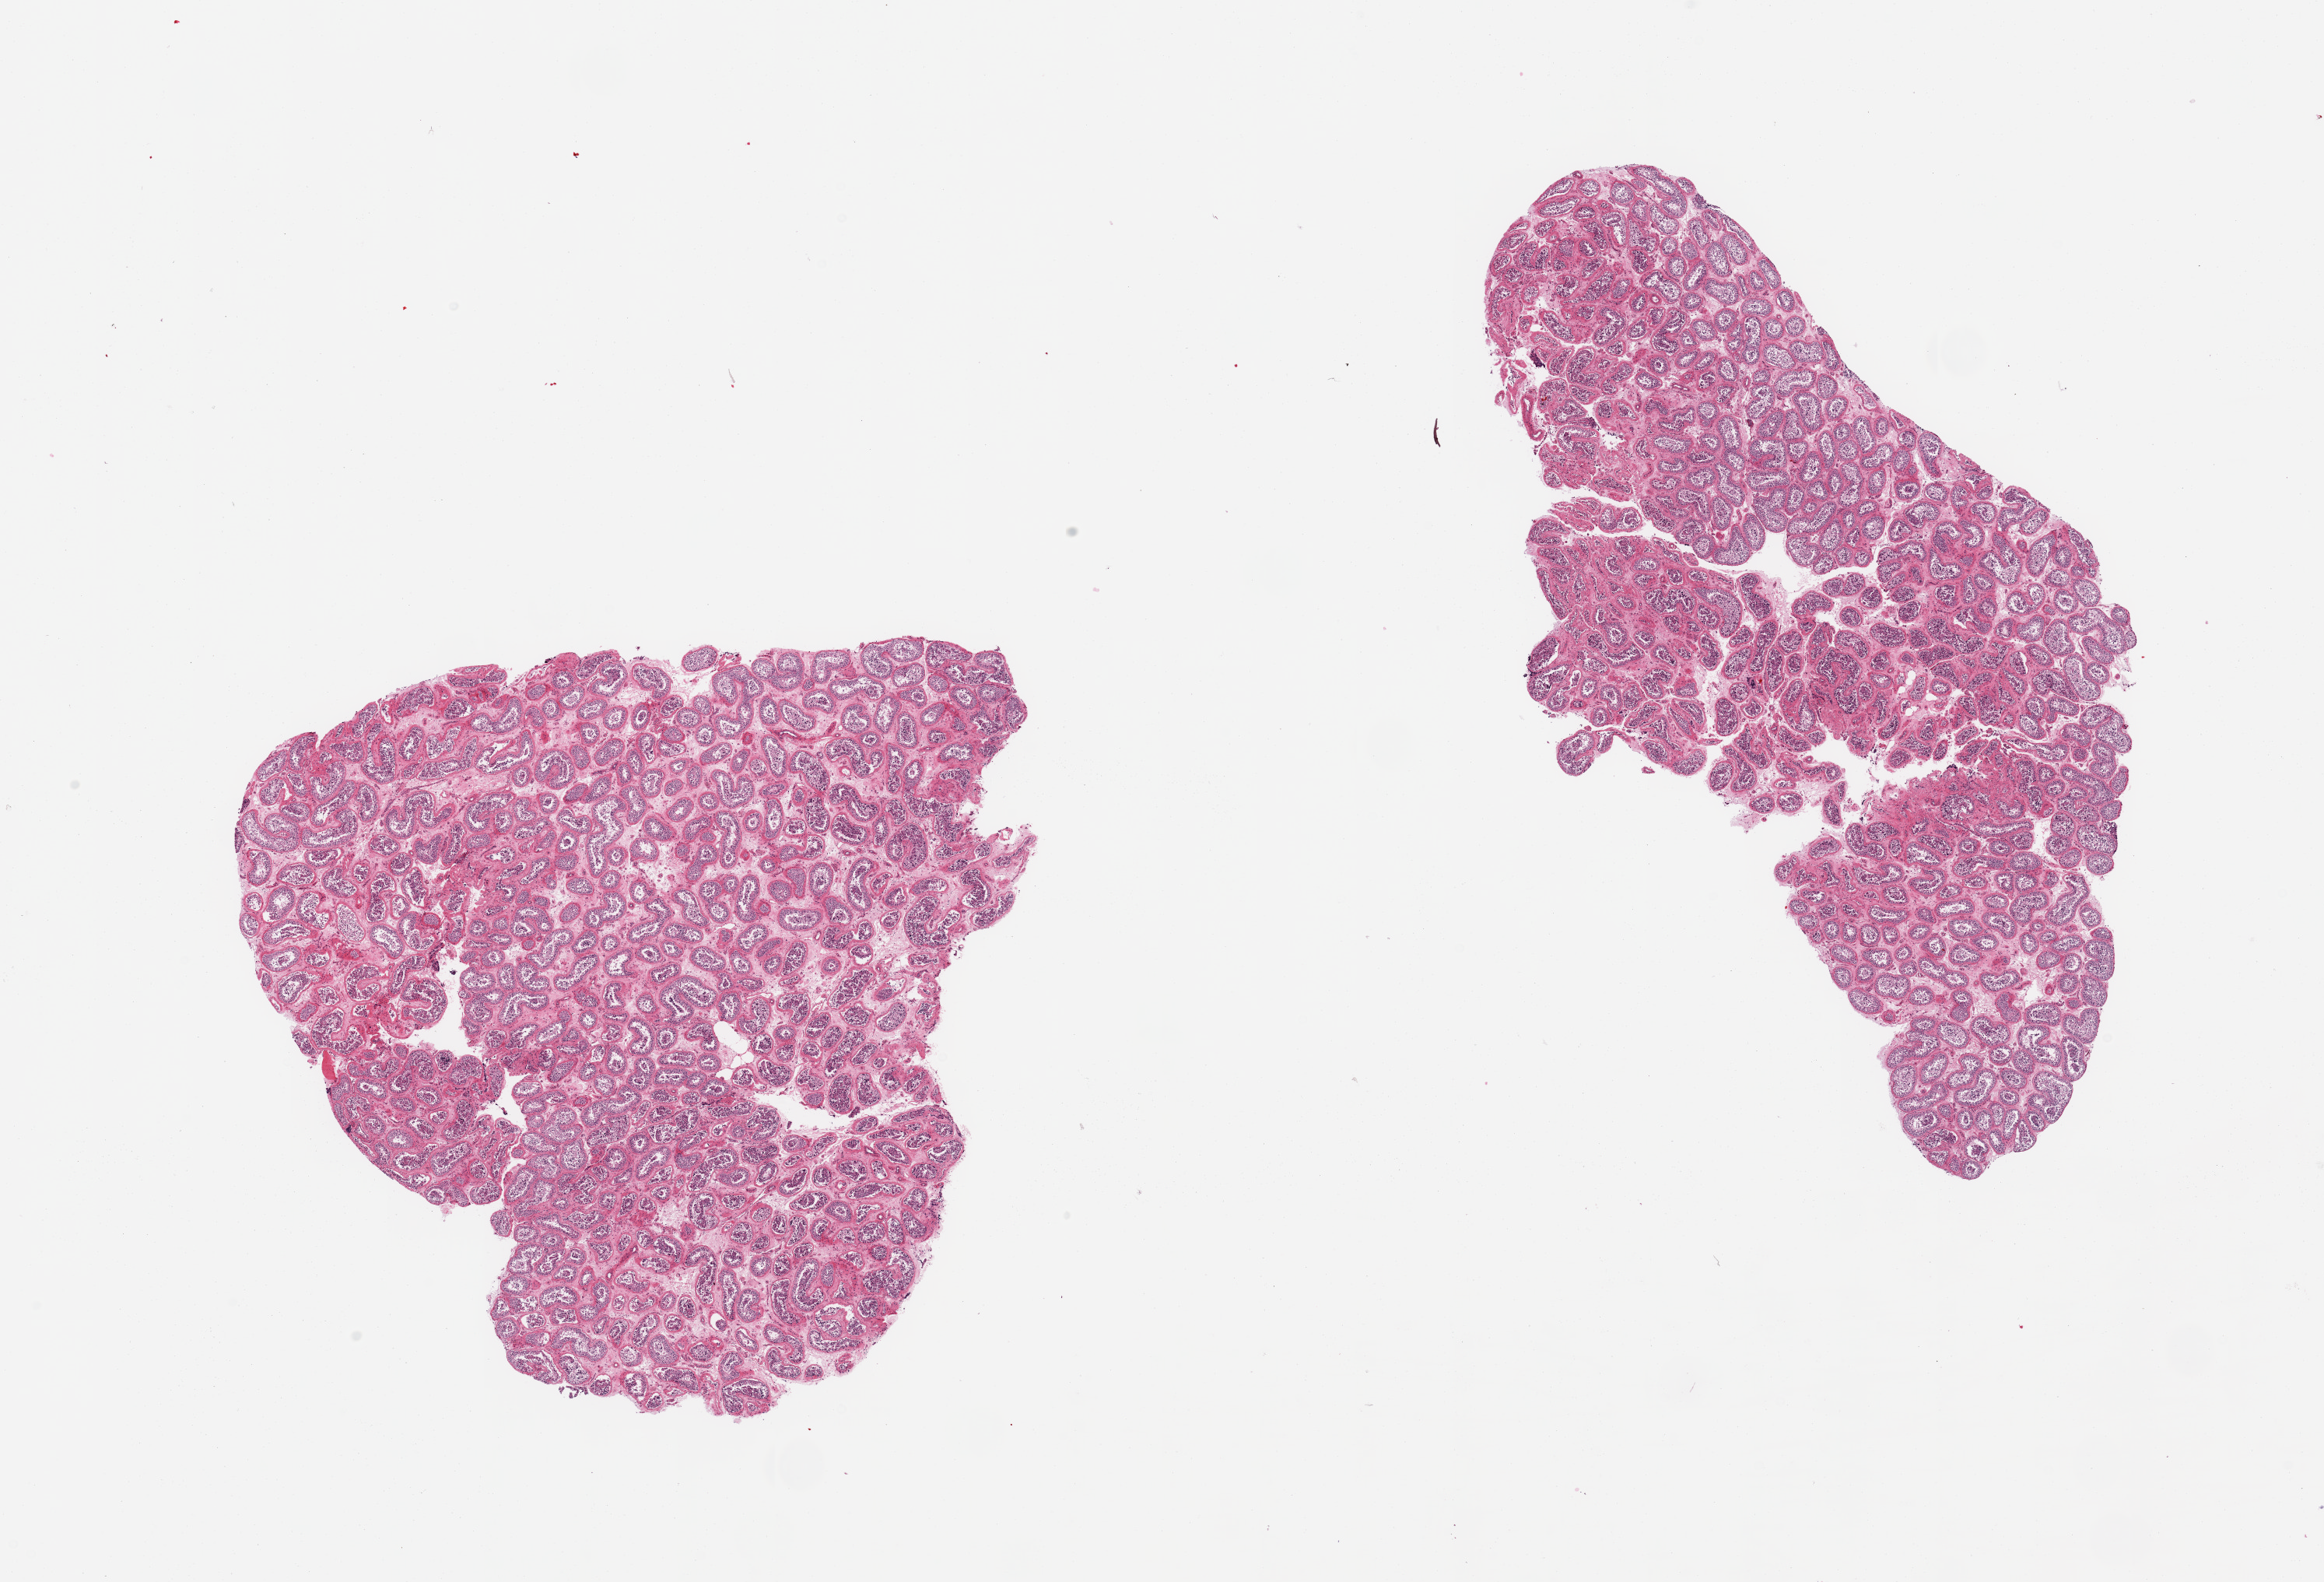
Hematoxylin and eosin (H&E) whole-slide image — low-resolution overview of the scanned area, about 23.6 x 16.1 mm (from a 20x scan), PAXgene-fixed paraffin-embedded (PFPE) section, target tissue: testis, donor tissue sample. Male donor.
• review note (as recorded): 2 pieces; active spermatogenesis